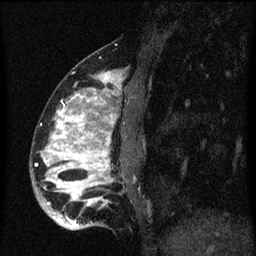
Breast MRI (dynamic contrast-enhanced), one sagittal slice; position 20 of 60 along the scan axis; dynamic contrast-enhanced series, image 2 of 3 at this slice position (ordered by acquisition); 1.5 T; TE 4.2 ms, TR 8.4 ms; 2 mm slice thickness; 256 × 256 image matrix, field of view 180 × 180 mm. Female patient, age 34 years. Case-level facts recorded for this patient, not image findings: setting: breast cancer imaged before/during neoadjuvant chemotherapy; receptor status: HR-positive, HER2-negative.
Annotated regions visible in this slice (semi-automatic segmentation, software-assisted and operator-edited):
- analysis volume of interest (the breast-tissue region the enhancement analysis was run in; not a lesion): bounding box (x1, y1, x2, y2) in pixels: (32, 58, 133, 231)
- tumour enhancement mask (voxels above the 70 % enhancement threshold inside the analysis volume of interest): (46, 74, 119, 227)